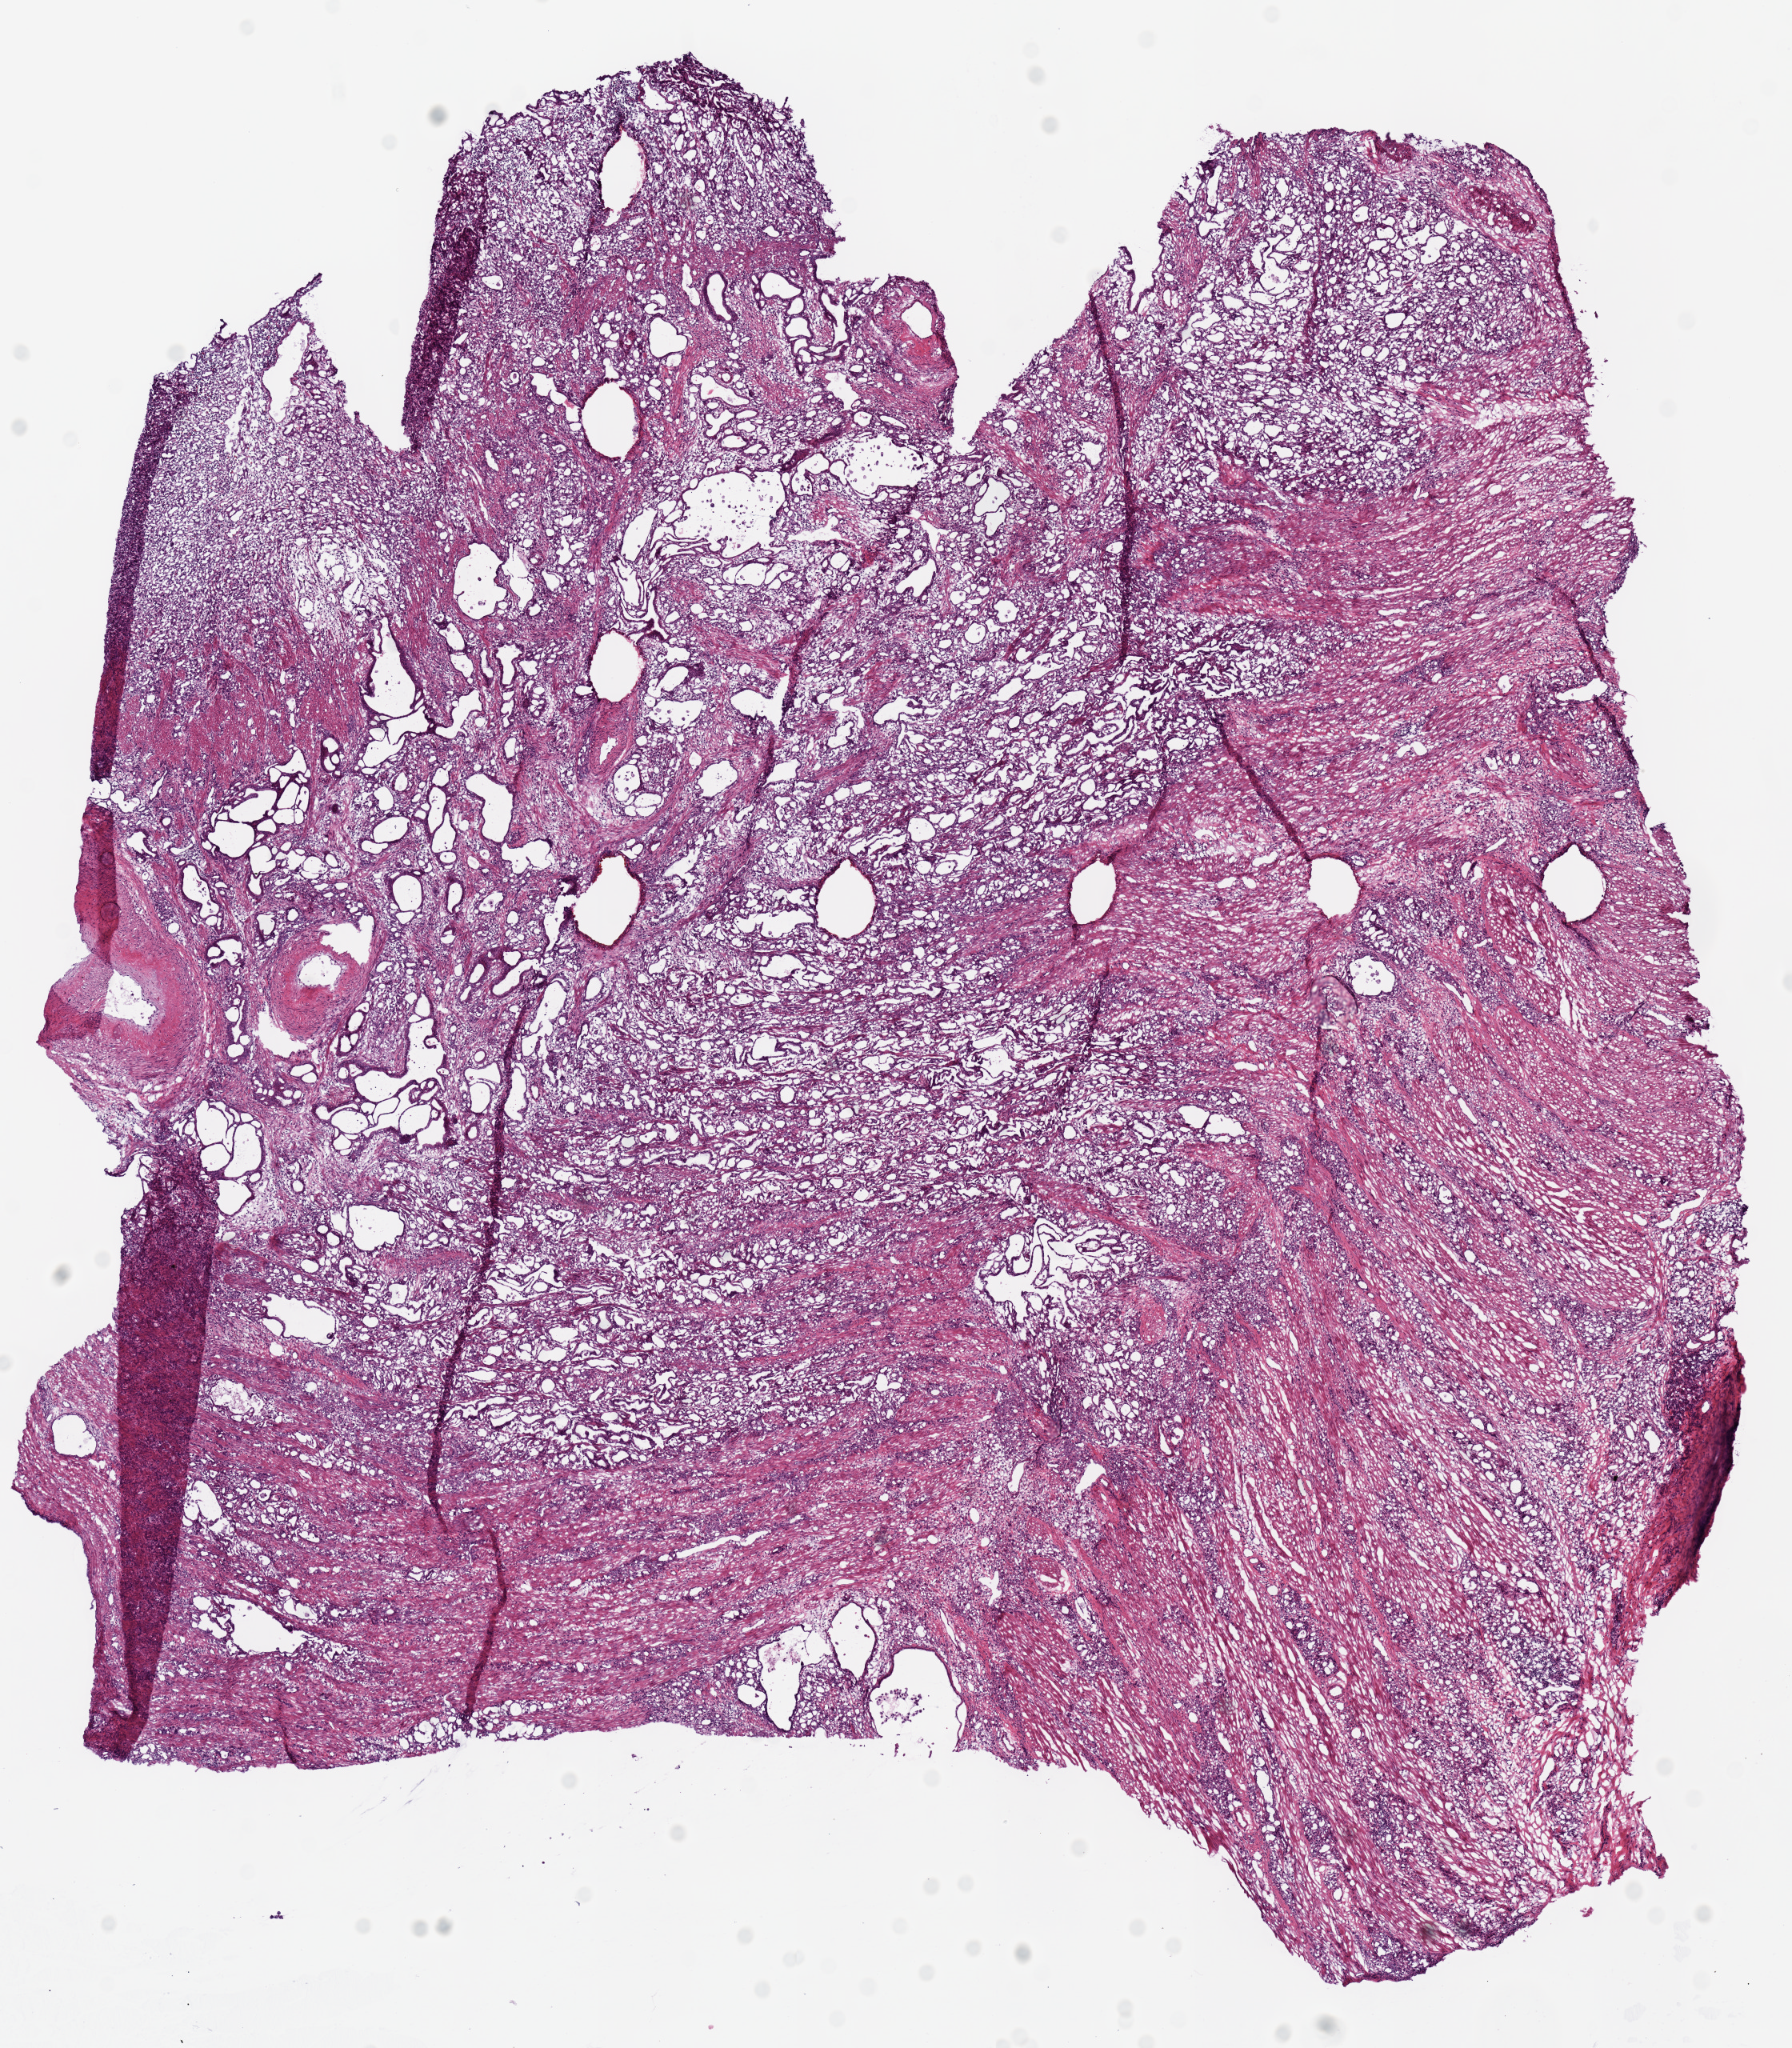
Digitized H&E tissue section (whole slide) — a low-resolution overview of the entire scanned area, about 8.9 x 10.1 mm (acquisition: 20x scan); frozen section; primary tumour sample from the stomach. Male patient; age at initial diagnosis 62 years. Composition of this section per pathologist review: tumour cells 90%, tumour nuclei 80%.
Pathologic diagnosis: Adenocarcinoma, NOS (cardia, NOS).